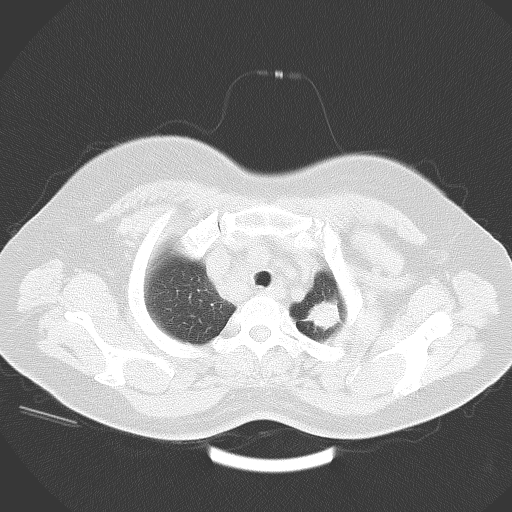
Chest CT, one axial slice; position 52 of 58 along the scan axis; lung window (W 1500 / L -600 HU); 5 mm slice thickness; 512 × 512 image matrix. Patient: female, 53 years. Case-level facts recorded for this patient, not image findings: clinical TNM (as recorded): T1c N3 M0.
Annotated regions visible in this slice (rectangle marked by the reading radiologist):
- lung tumour (recorded histology: adenocarcinoma): bounding box <304,297,342,337> (left, top, right, bottom; pixels)